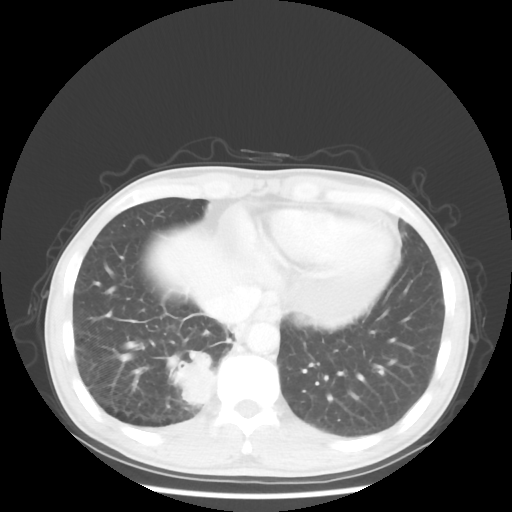
Chest CT, one axial slice. Slice 12 of 58 in the series (ordered by position). 100 kVp. Lung window (W 1500 / L -600 HU). 5 mm slice thickness. 512 × 512 image matrix. Patient: male, 56 years. From the clinical record (not read from this slice): clinical TNM (as recorded): T2 N1 M1; histopathological grade: G1.
Outlined on this slice (rectangle marked by the reading radiologist):
- lung tumour (recorded histology: adenocarcinoma): bounding box [x1, y1, x2, y2] px = [168, 352, 216, 406]